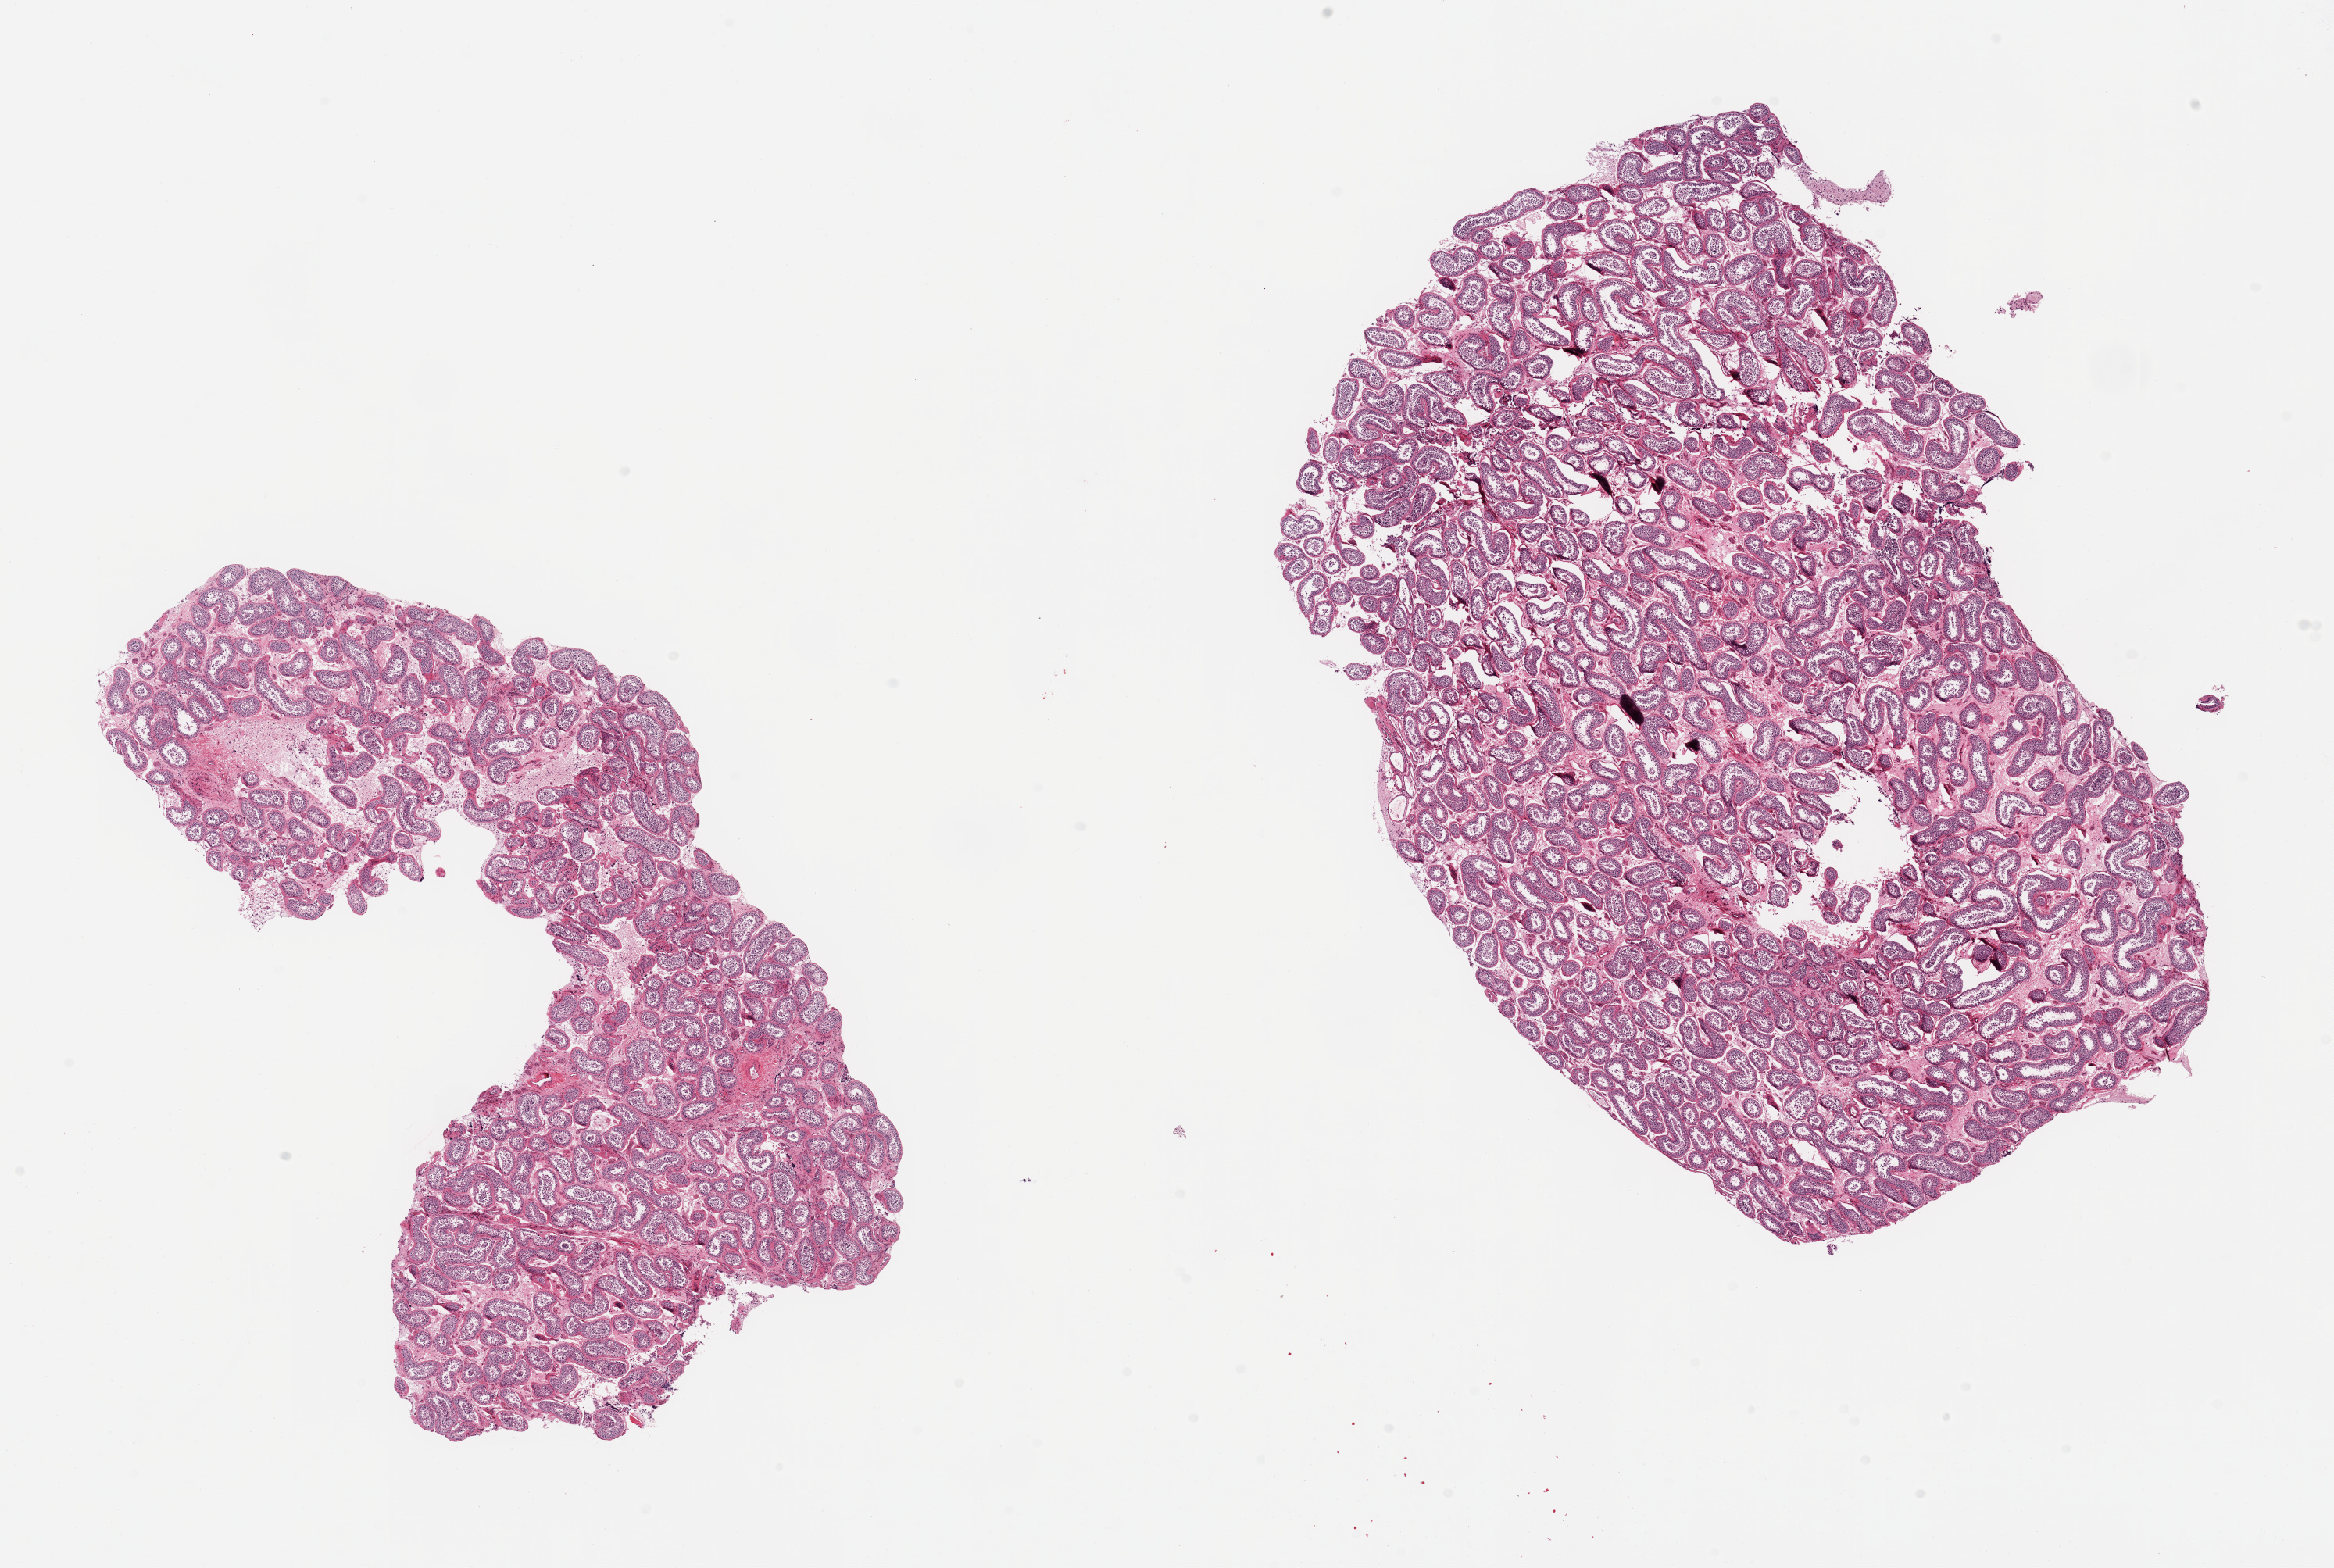
H&E whole-slide image, a low-resolution overview of the entire scanned area, about 23.6 x 15.9 mm. PAXgene-fixed, paraffin-embedded tissue. Section of testis (target tissue). Tissue donor sample. Male donor.
Review note (as recorded): 2 pieces, spermatogenesis is present.